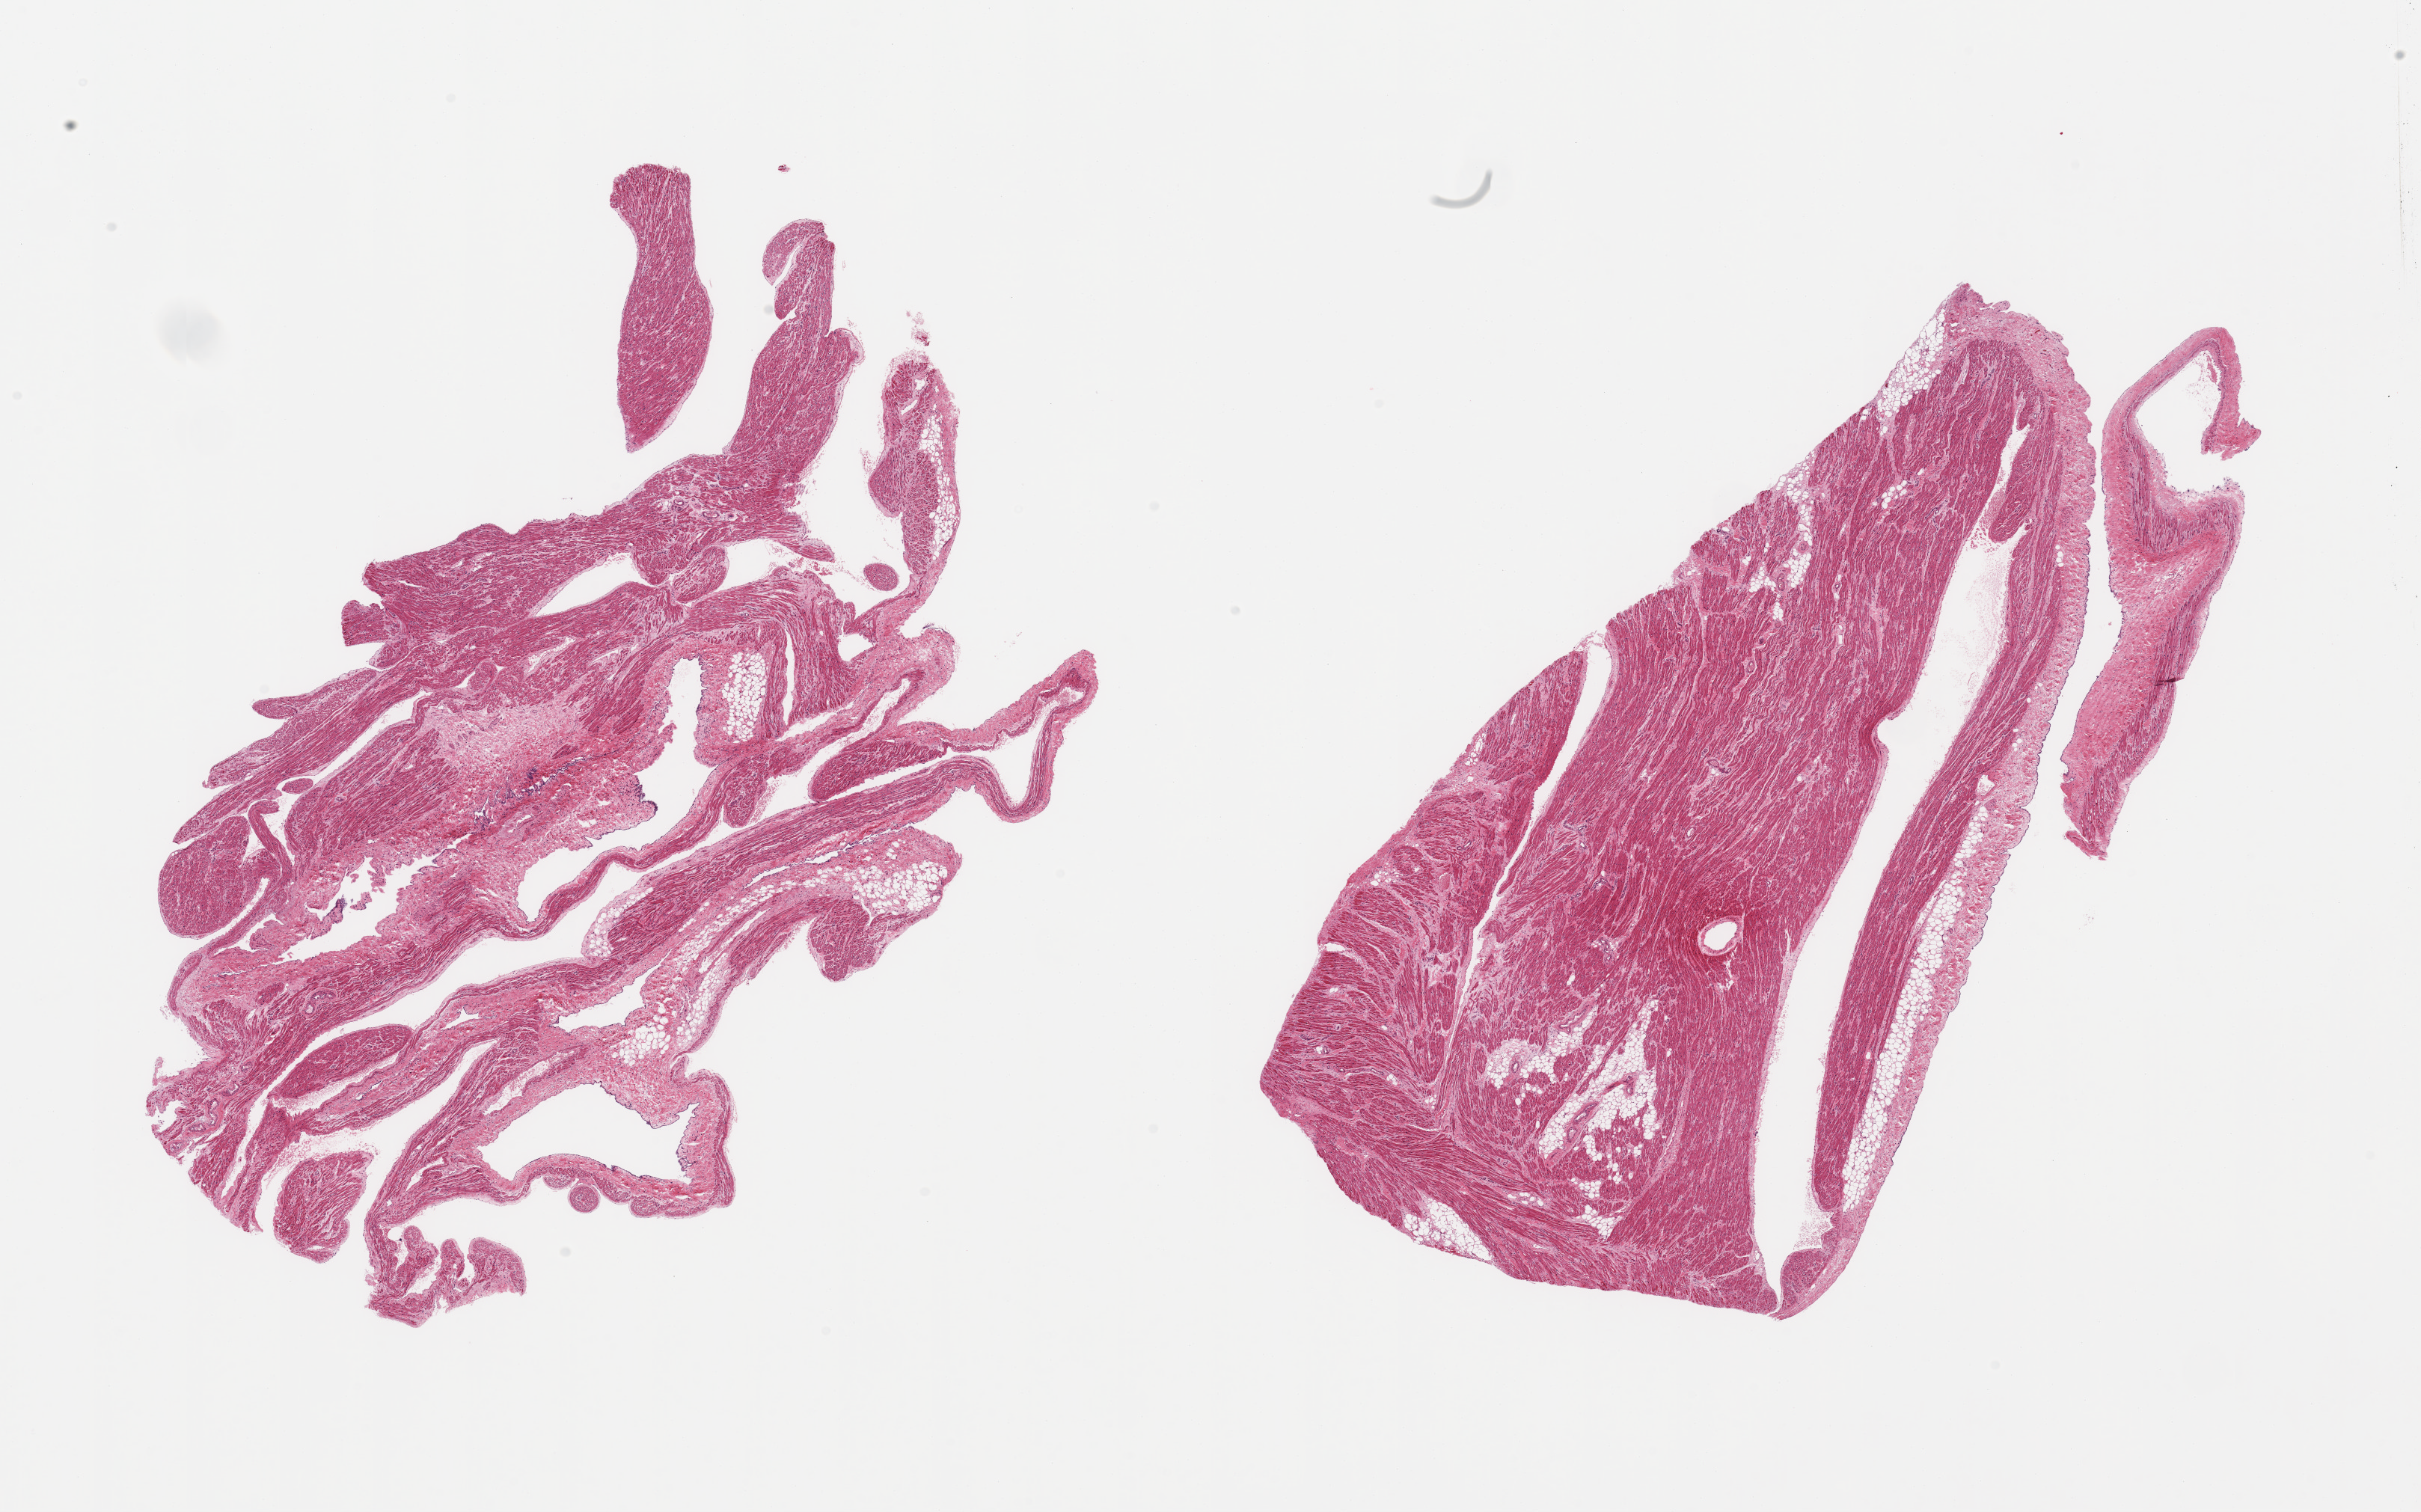
Whole-slide image, H&E stain, low-resolution overview of the scanned area, about 25.6 x 16.0 mm (slide scanned at 20x), PAXgene-fixed, paraffin-embedded tissue, target tissue: auricular appendage, tissue donor sample. Donor: female.
Pathologist's review note for this sample: 2 pieces; larger piece with 20% fibroadipose content; smaller with 60%.